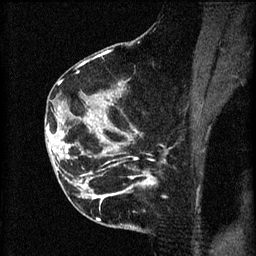
Breast MRI (dynamic contrast-enhanced), one sagittal slice; slice 29 of 60 in the series (ordered by position); 3 images stored at this slice position (order not interpretable as contrast timing); 1.5 T; TE 4.2 ms, TR 8.2 ms; 2 mm slice thickness; 256 × 256 image matrix, field of view 180 × 180 mm. Female patient, age 49 years.
Annotated regions visible in this slice (semi-automatic segmentation, software-assisted and operator-edited):
- analysis volume of interest (the breast-tissue region the enhancement analysis was run in; not a lesion): bounding box (x1, y1, x2, y2) in pixels: (45, 126, 105, 177)
- tumour enhancement mask (voxels above the 70 % enhancement threshold inside the analysis volume of interest): (46, 126, 105, 159)